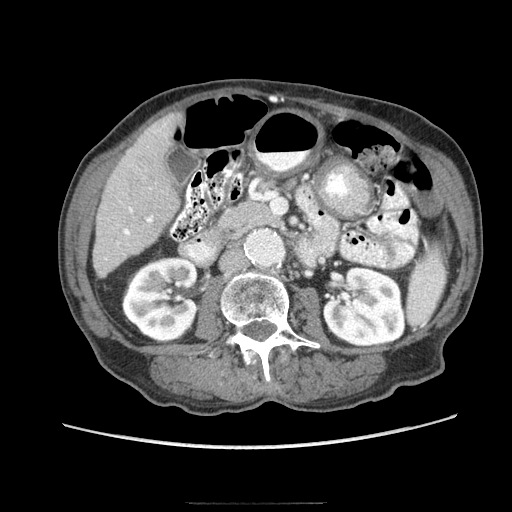
Contrast-enhanced abdominal CT (liver protocol), one axial slice. Position 27 of 83 along the scan axis. Reconstruction kernel STANDARD. 140 kVp. Soft-tissue window (W 400 / L 40 HU). 2.5 mm slice thickness. 512 × 512 image matrix. Case-level facts recorded for this patient, not image findings: diagnosis: hepatocellular carcinoma (patient treated with transarterial chemoembolisation; whether this scan precedes or follows treatment is not stated here); TNM stage (as recorded): Stage-I; Child-Pugh class: A; tumour differentiation: moderately differentiated.
Annotated regions visible in this slice (semi-automatically segmented with operator editing):
- liver parenchyma outside the tumour (the mass and vessels are separate outlines, so this box may not span the whole liver): box from (x=92, y=112) to (x=182, y=277) px
- liver vessels: (x=118, y=208)–(x=152, y=244)